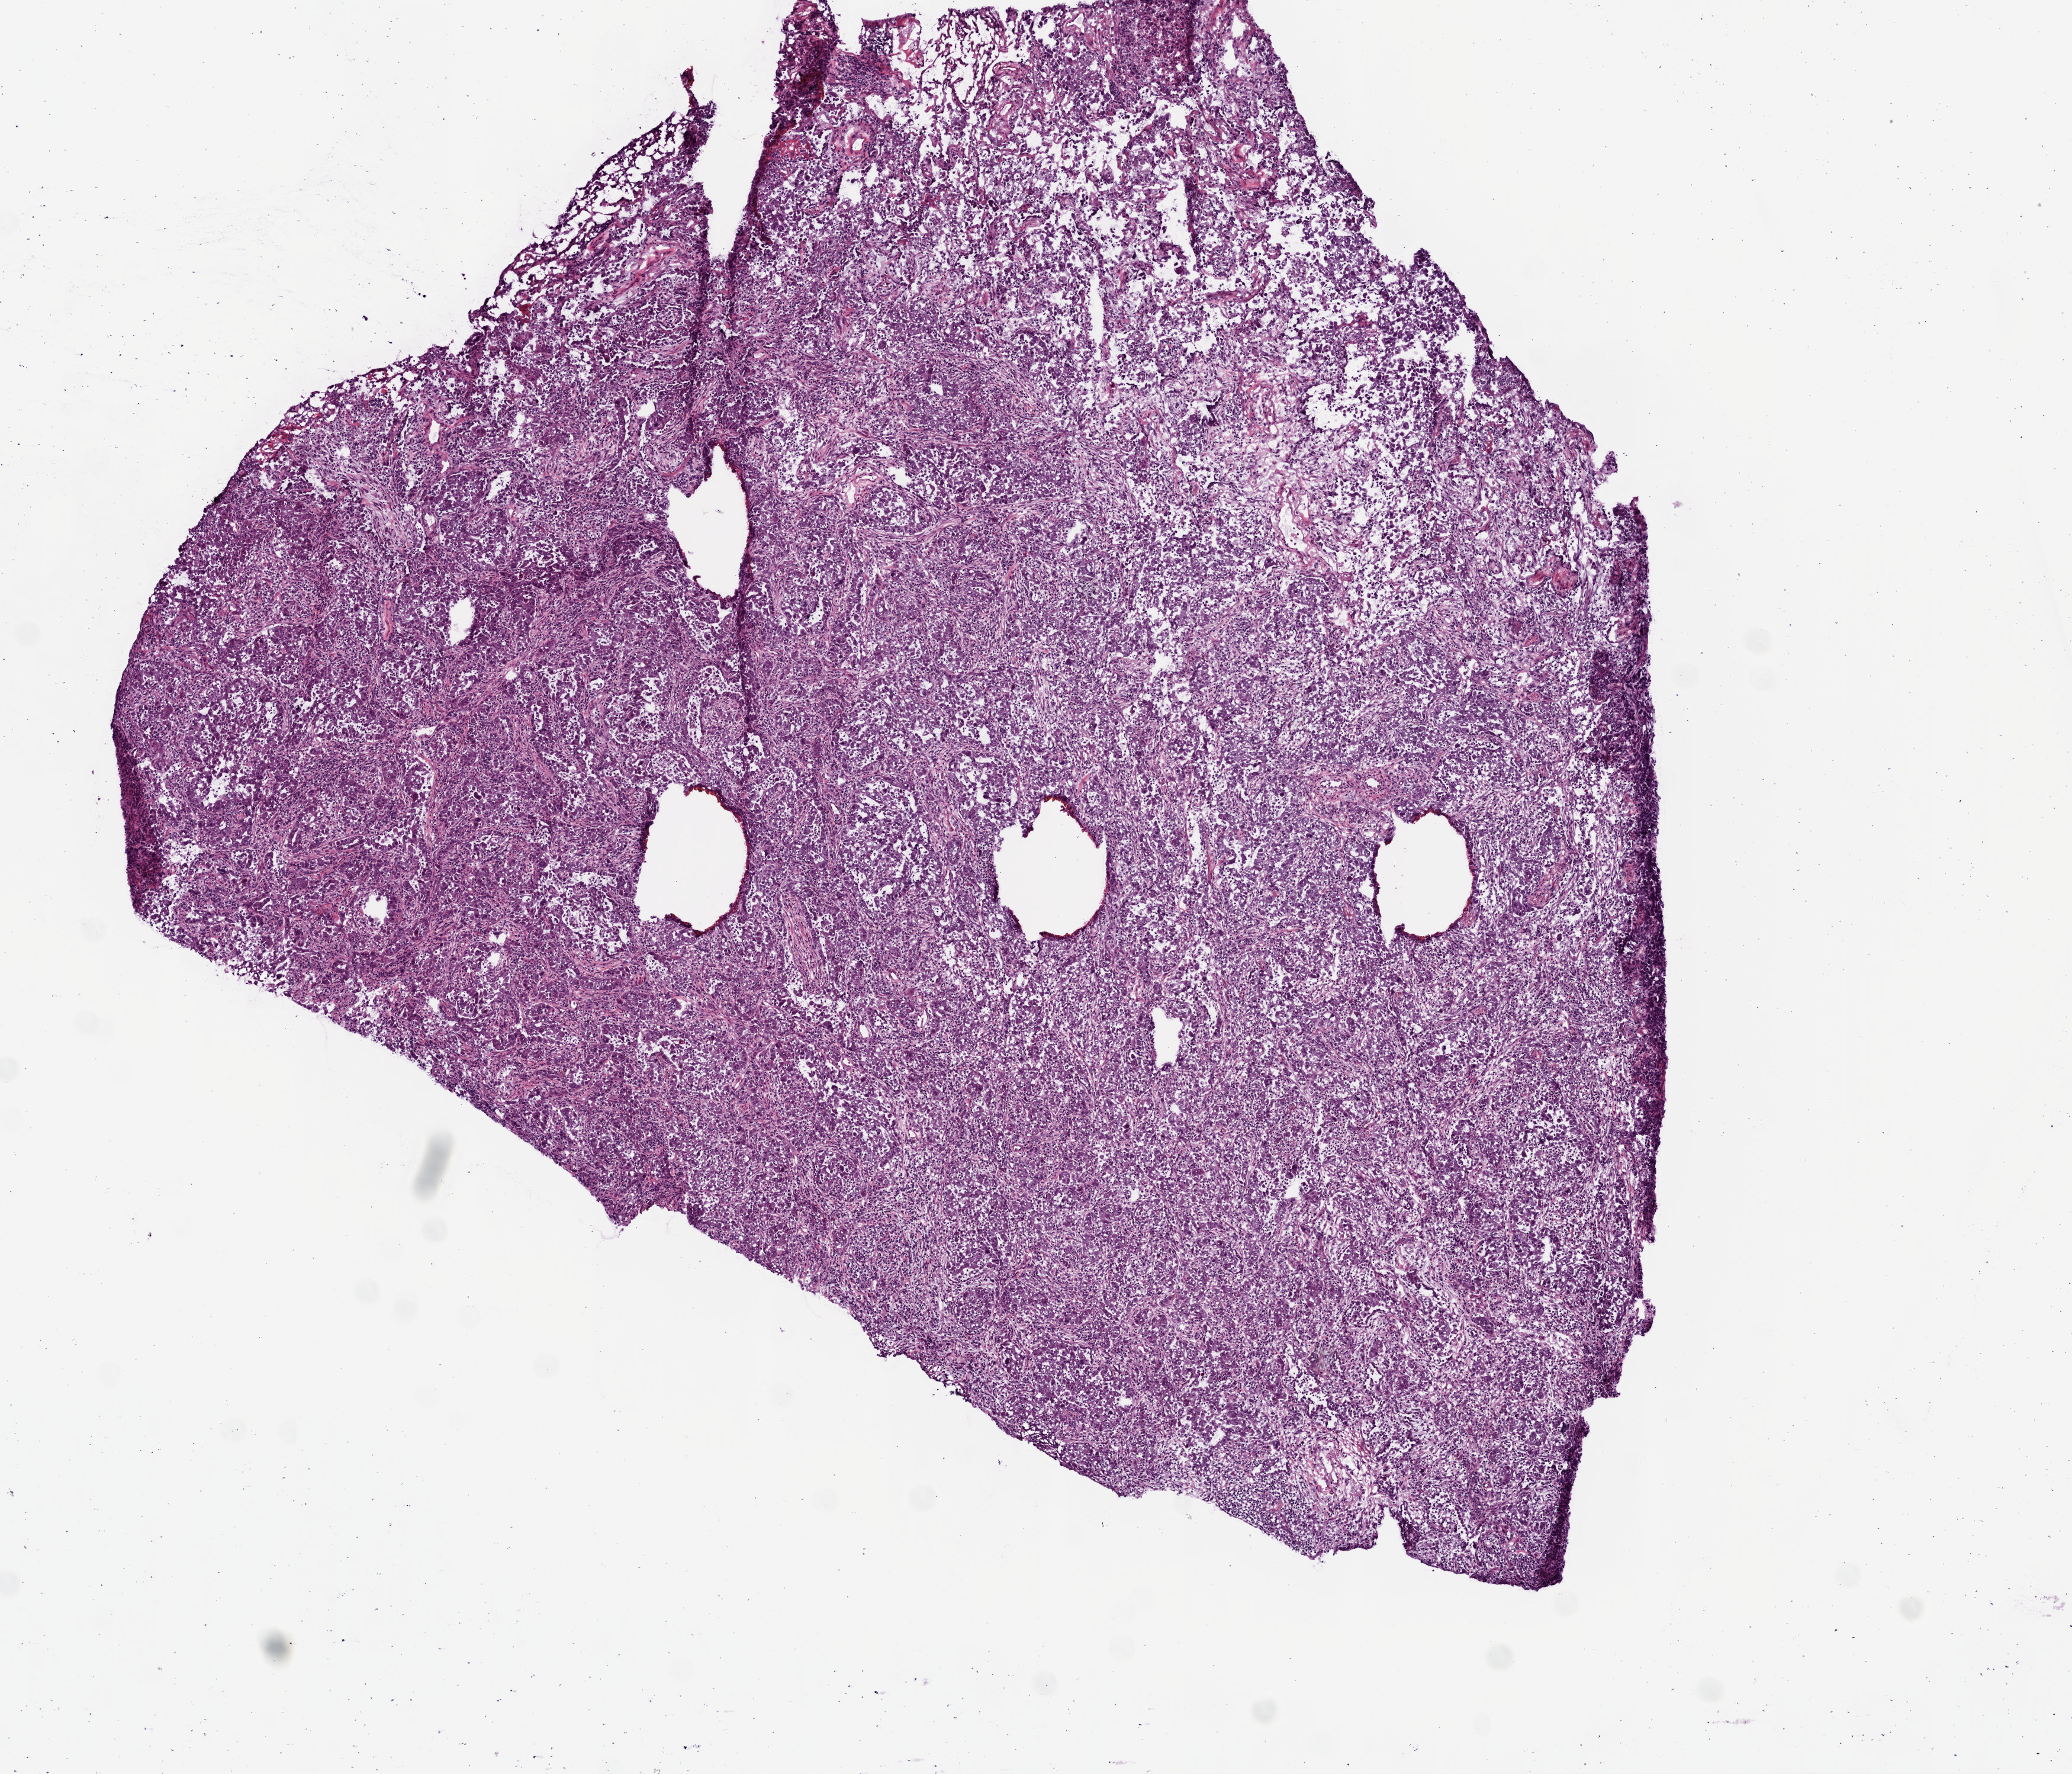
Whole-slide histology image, H&E — a low-resolution overview of the entire scanned area, about 7.0 x 6.0 mm (slide scanned at 20x), frozen section from the top of the tissue portion, primary tumour sample from the lung. Patient: female, age at initial diagnosis 74 years. Composition of this section per pathologist review: tumour cells 79%, tumour nuclei 60%, normal cells 0%, stromal cells 20%, necrosis 1%.
AJCC pathologic stage: IV (7th edition). Laterality: right. Pathologic diagnosis: Adenocarcinoma, NOS (upper lobe, lung).